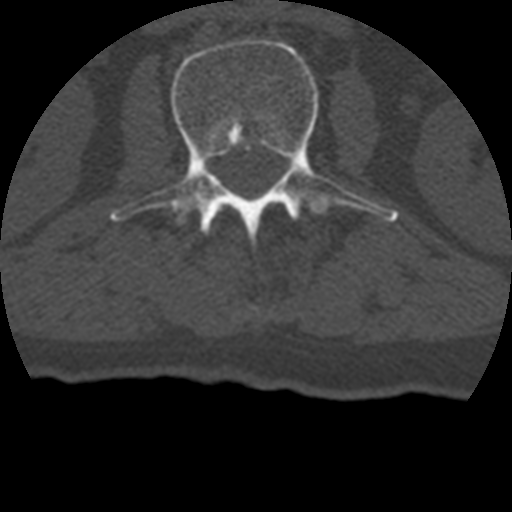
CT including the spine, one axial slice; slice 119 of 399 in the series (ordered by position); bone window (W 1800 / L 400 HU); 1.25 mm slice thickness; 512 × 512 image matrix, field of view 160 × 160 mm. Patient age 69 years. Case-level facts recorded for this patient, not image findings: primary cancer: prostate.
Outlined on this slice (semi-automatic segmentation, software-assisted and operator-edited):
- L2 vertebra: box from (x=111, y=39) to (x=398, y=252) px